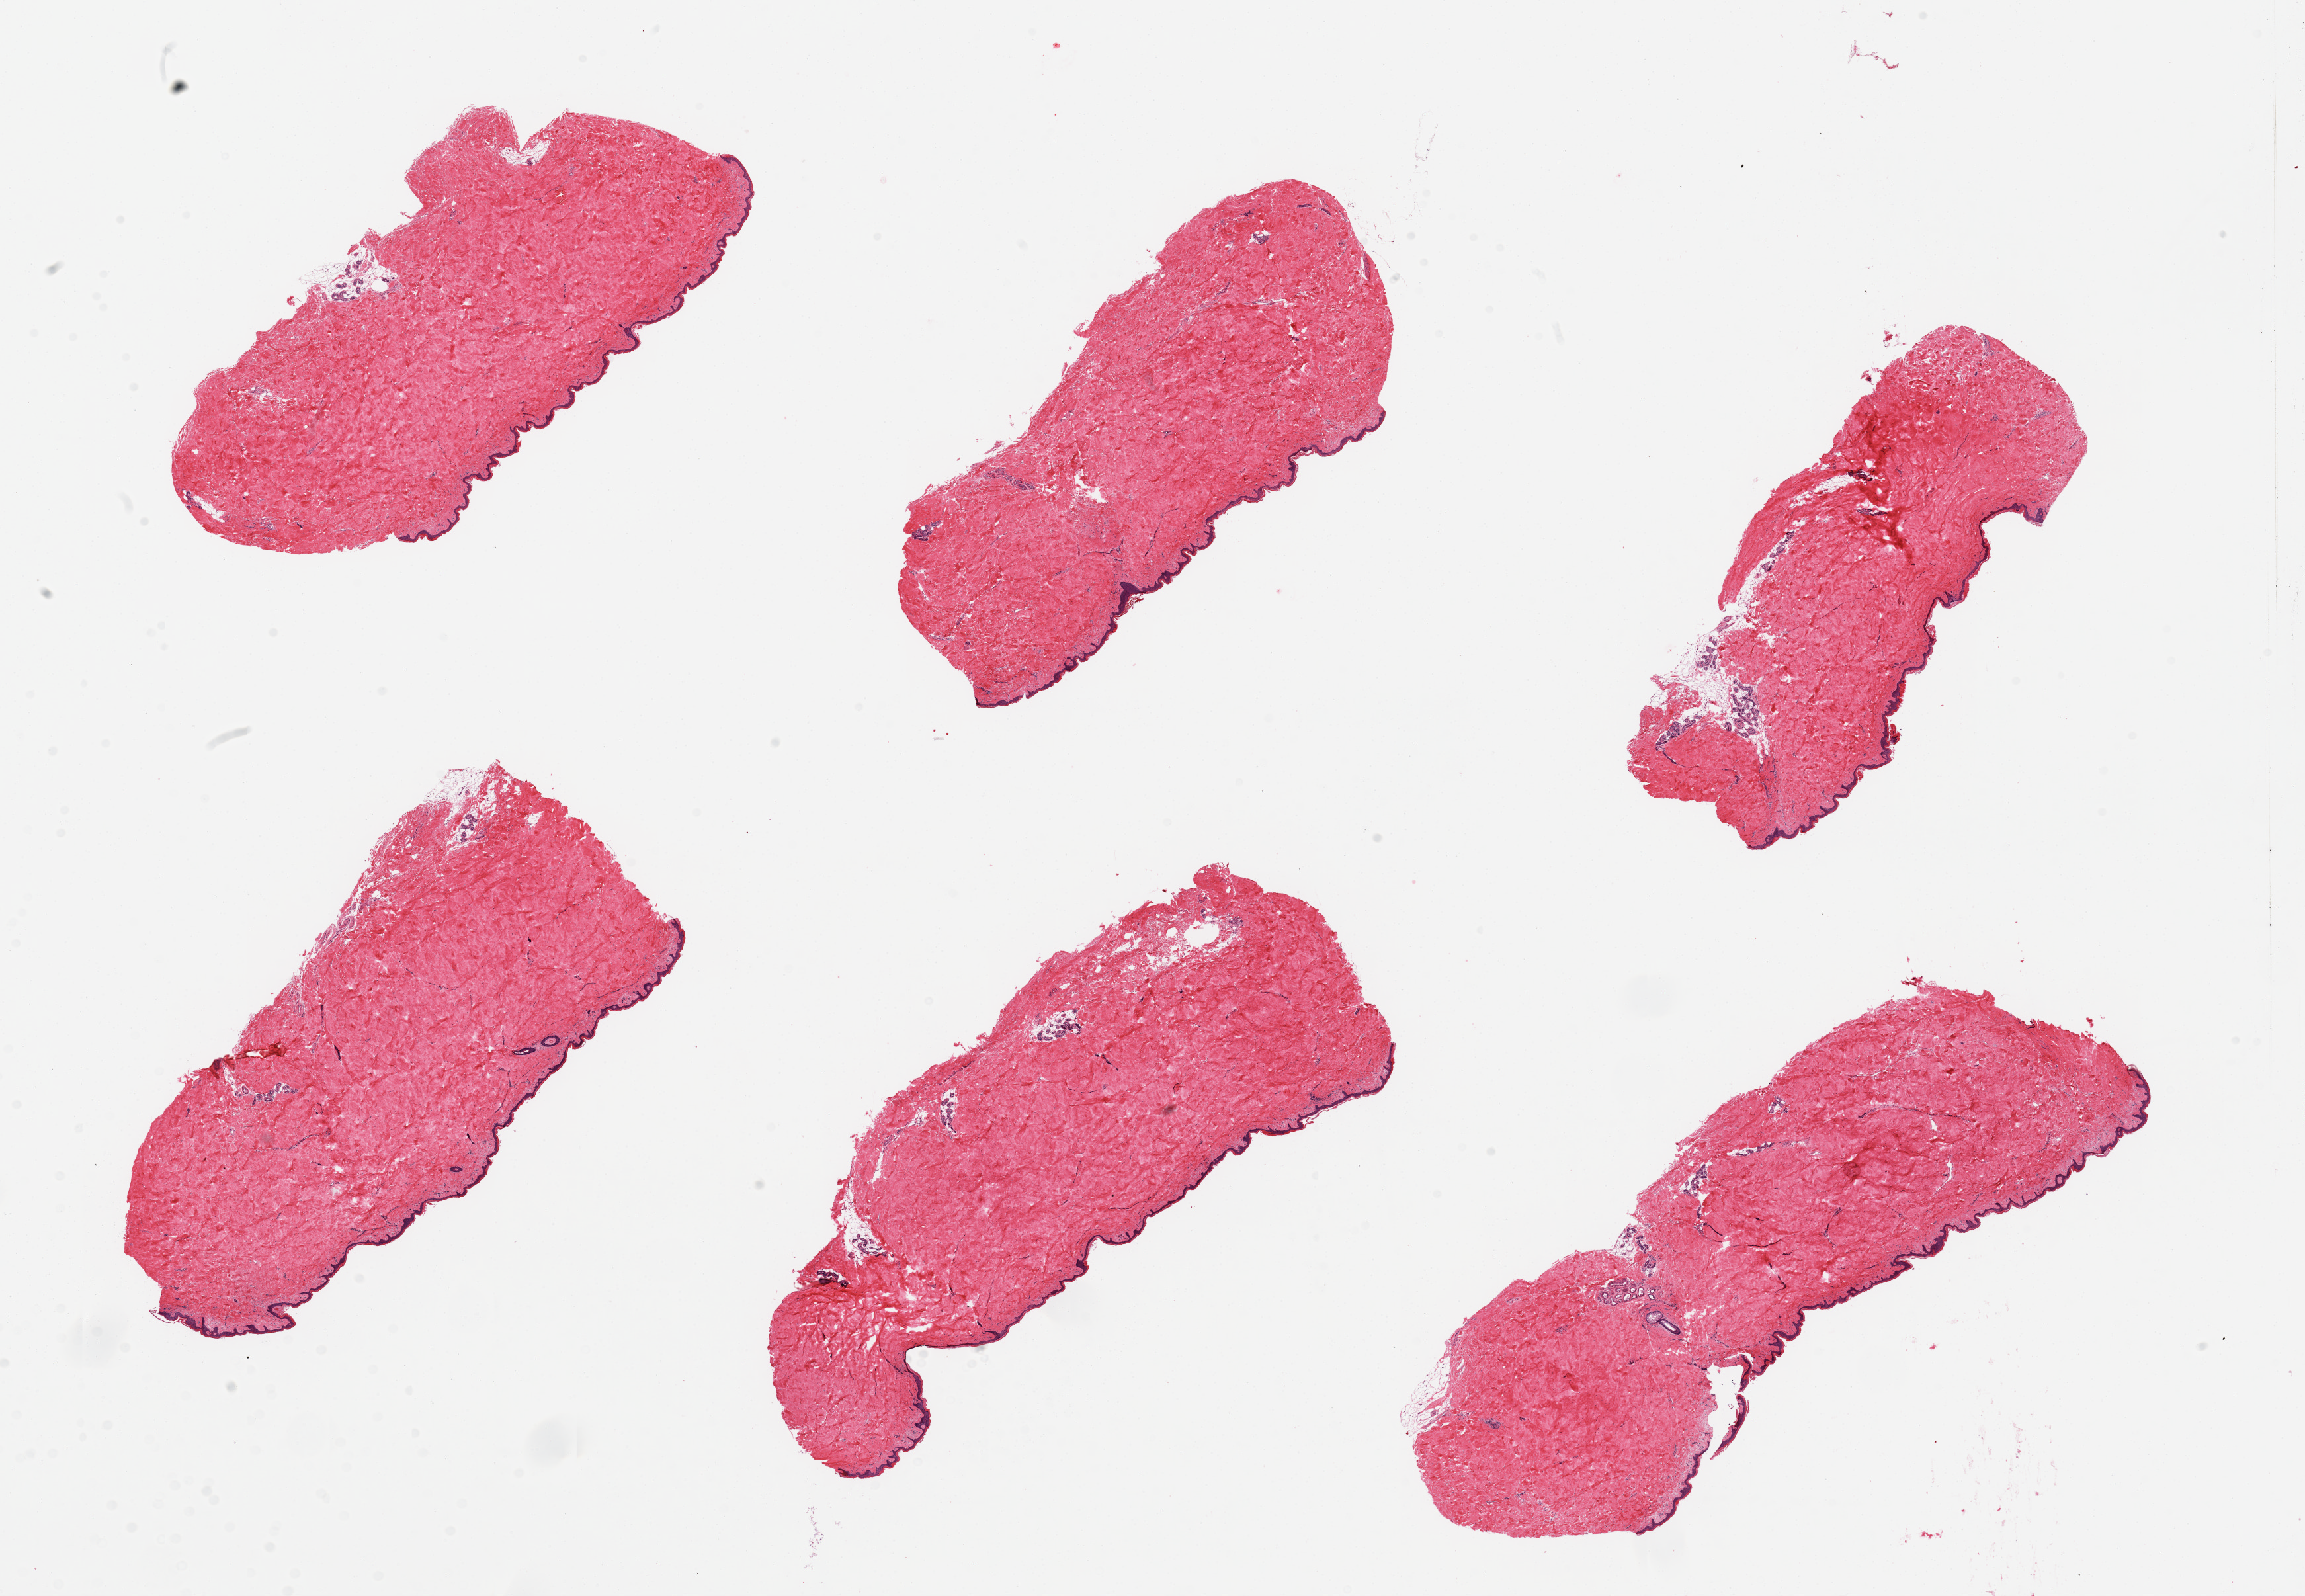
Whole-slide image, H&E stain, a low-resolution overview of the entire scanned area, about 27.6 x 19.1 mm. PAXgene-fixed paraffin-embedded (PFPE) section. Target tissue: skin of suprapubic region. Donor tissue sample.
Review note (as recorded): 2 pieces, no dermal fat; squamous epithelium is ~45 microns.